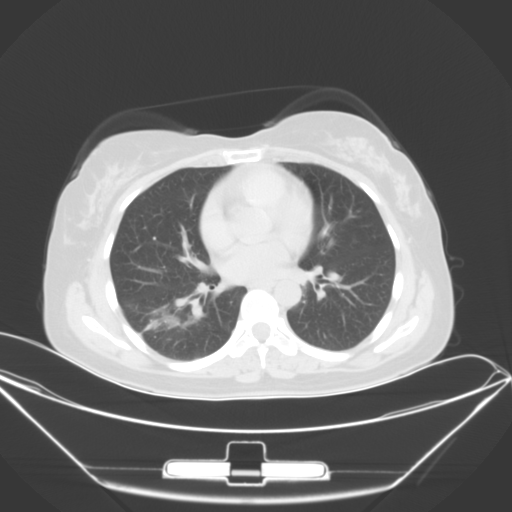
Chest CT, one axial slice; position 19 of 46 along the scan axis; 120 kVp; lung window (W 1500 / L -600 HU); 512 × 512 image matrix, field of view 407 × 407 mm. Patient: female, 42 years. Case-level facts recorded for this patient, not image findings: clinical TNM (as recorded): T1c N0 M1a.
Structures marked on this image (bounding box drawn by a radiologist):
- lung tumour (recorded histology: adenocarcinoma): box from (x=143, y=303) to (x=191, y=336) px